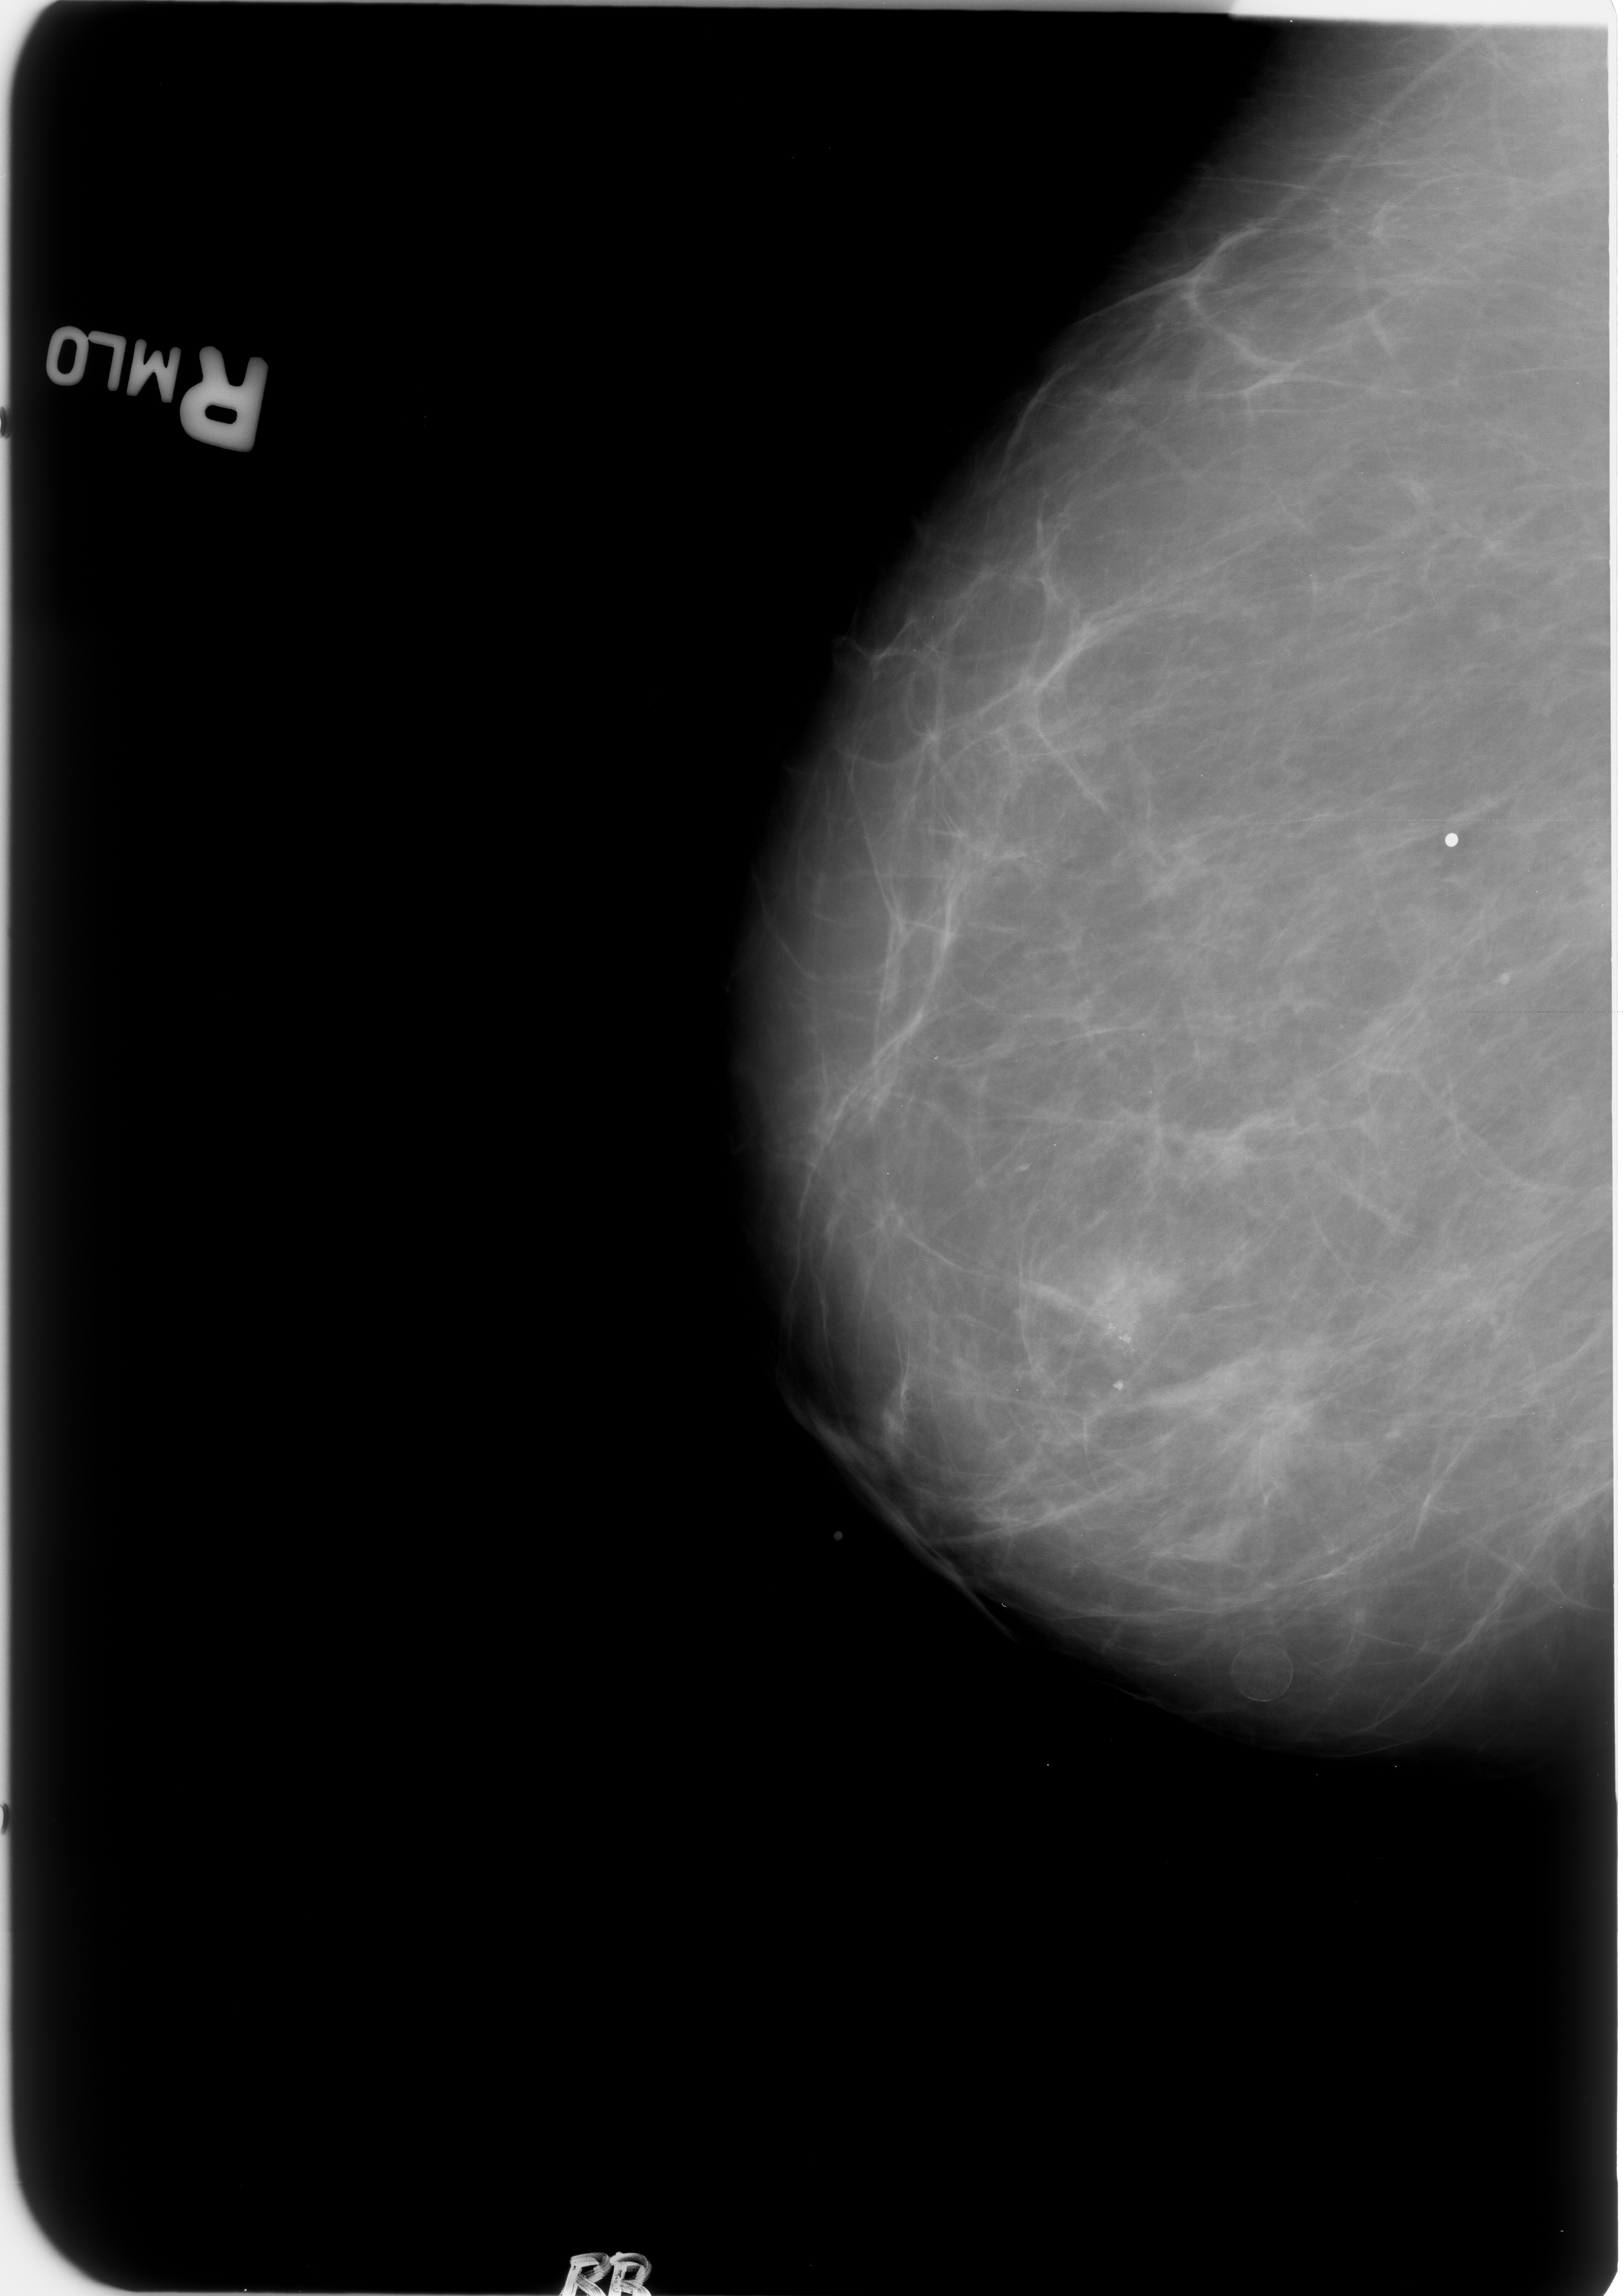
Digitized screen-film mammogram; right breast; mediolateral oblique (MLO) view; BI-RADS breast density category 1 (scale 1–4).
Marked findings (only marked abnormalities are described; nothing is implied about the rest of the image): calcifications, morphology pleomorphic, distribution clustered; BI-RADS assessment category 4; subtlety rating 4 on a 1 (subtle) to 5 (obvious) scale; pathology (as recorded): benign.